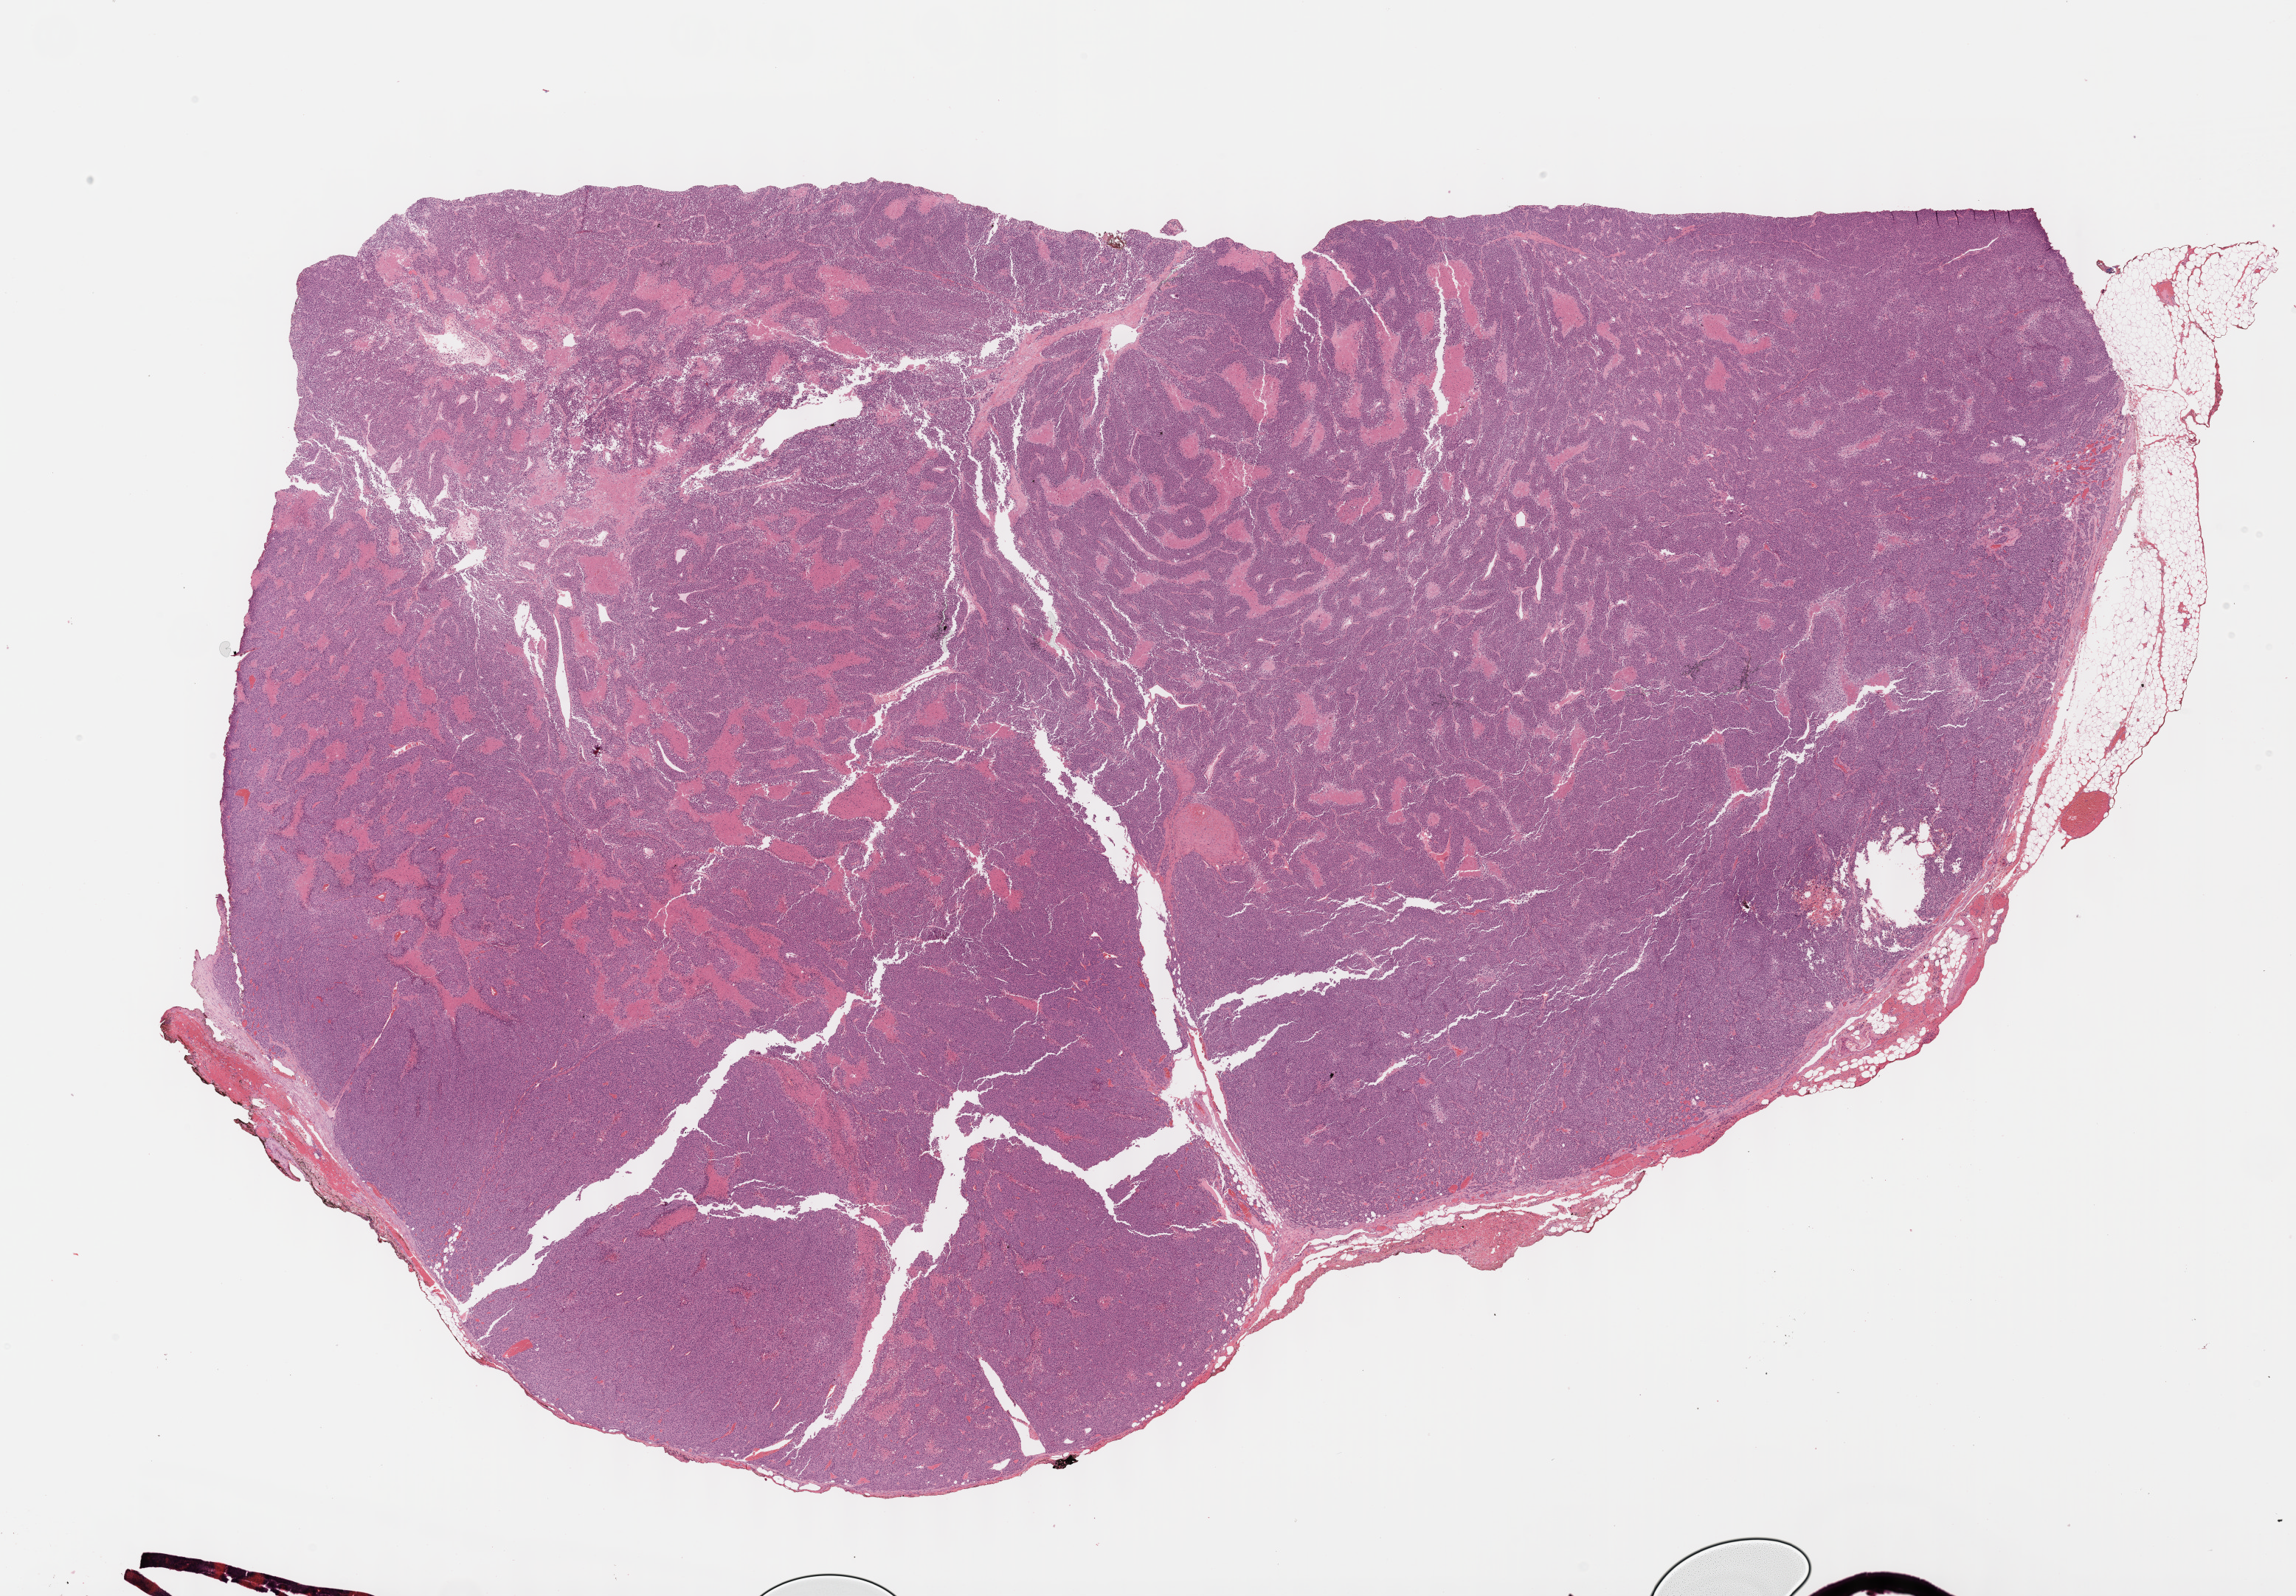
Whole-slide histology image, H&E-stained — low-resolution overview of the scanned area, about 25.1 x 17.5 mm. Formalin-fixed paraffin-embedded (FFPE) diagnostic section. Adrenal cortex, primary tumour sample. Female, age 25 years at initial diagnosis.
Histologic diagnosis: Adrenal cortical carcinoma (cortex of adrenal gland).